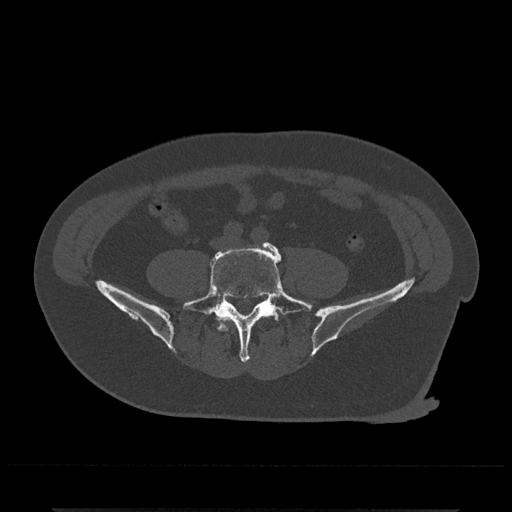
CT including the spine, one axial slice; slice 92 of 797 in the series (ordered by position); reconstruction kernel Br40s/3; 120 kVp; bone window (W 1800 / L 400 HU); 0.5 mm slice thickness; 512 × 512 image matrix, field of view 393 × 393 mm. Male patient, age 67 years. From the clinical record (not read from this slice): primary cancer: prostate.
Structures marked on this image (semi-automatic segmentation, software-assisted and operator-edited):
- L4 vertebra: bounding box [x1, y1, x2, y2] px = [221, 325, 229, 331]
- L5 vertebra: [182, 241, 313, 363]